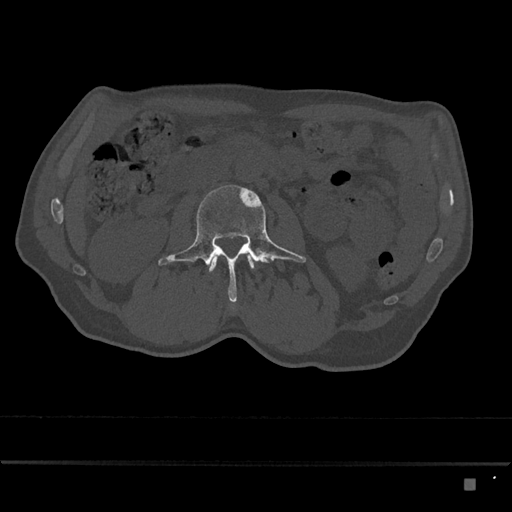
CT including the spine, one axial slice. Position 419 of 797 along the scan axis. Reconstruction kernel Br40s/3. 120 kVp. Bone window (W 1800 / L 400 HU). 0.5 mm slice thickness. 512 × 512 image matrix. Patient: male, 72 years. Case-level facts recorded for this patient, not image findings: primary cancer: prostate.
Structures marked on this image (semi-automatic segmentation, software-assisted and operator-edited):
- L2 vertebra: bounding box (x1, y1, x2, y2) in pixels: (209, 255, 254, 272)
- L3 vertebra: (158, 185, 306, 303)